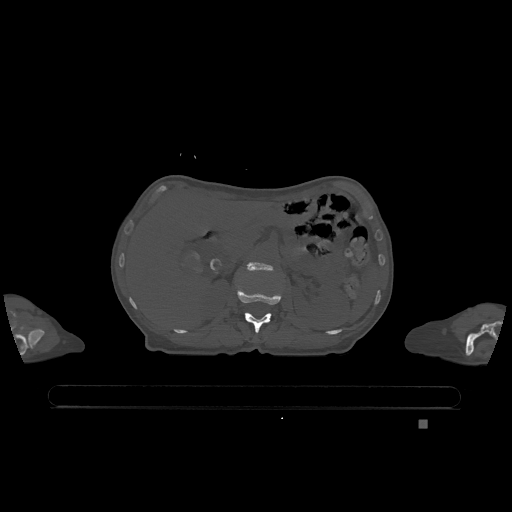
CT including the spine, one axial slice; slice 465 of 1317 in the series (ordered by position); bone window (W 1800 / L 400 HU); 0.5 mm slice thickness; 512 × 512 image matrix. Patient: female, 74 years. From the clinical record (not read from this slice): primary cancer: lung.
Outlined on this slice (semi-automatically segmented with operator editing):
- L1 vertebra: box from (x=237, y=285) to (x=282, y=333) px
- L2 vertebra: (x=247, y=262)–(x=273, y=271)